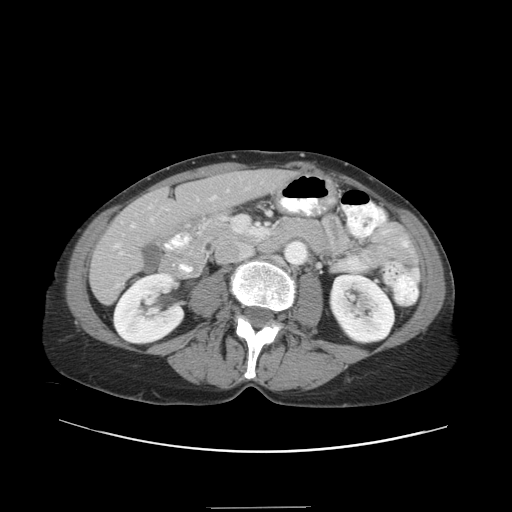
Contrast-enhanced abdominal CT, one axial slice; position 11 of 38 along the scan axis; reconstruction kernel STANDARD; 120 kVp; intravenous contrast given; soft-tissue window (W 400 / L 40 HU); 5 mm slice thickness; 512 × 512 image matrix. Female patient, age 64 years. Case-level facts recorded for this patient, not image findings: diagnosis: colorectal cancer liver metastases, imaged before liver resection; multiple liver metastases: no; largest metastasis: 3.8 cm; disease in both lobes: yes.
Outlined on this slice (manually delineated by an expert):
- hepatic veins: bounding box (x1, y1, x2, y2) in pixels: (115, 195, 217, 248)
- liver: (92, 171, 289, 302)
- planned liver remnant (the part of the liver to remain after resection): (159, 171, 289, 223)
- portal vein (with intrahepatic branches): (119, 189, 229, 255)